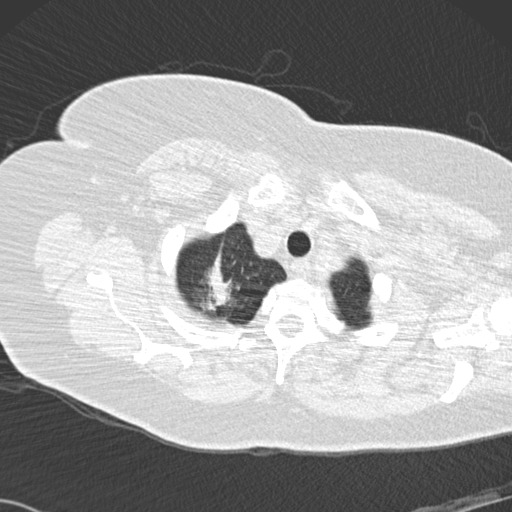
Low-dose screening chest CT, one axial slice; reconstruction kernel B30f; lung window (W 1500 / L -600 HU); 2 mm slice thickness; 512 × 512 image matrix.
Structures marked on this image (outlined manually by an expert reader):
- lesion 1 (tumor, upper lobe of right lung): bounding box <200,254,232,311> (left, top, right, bottom; pixels)